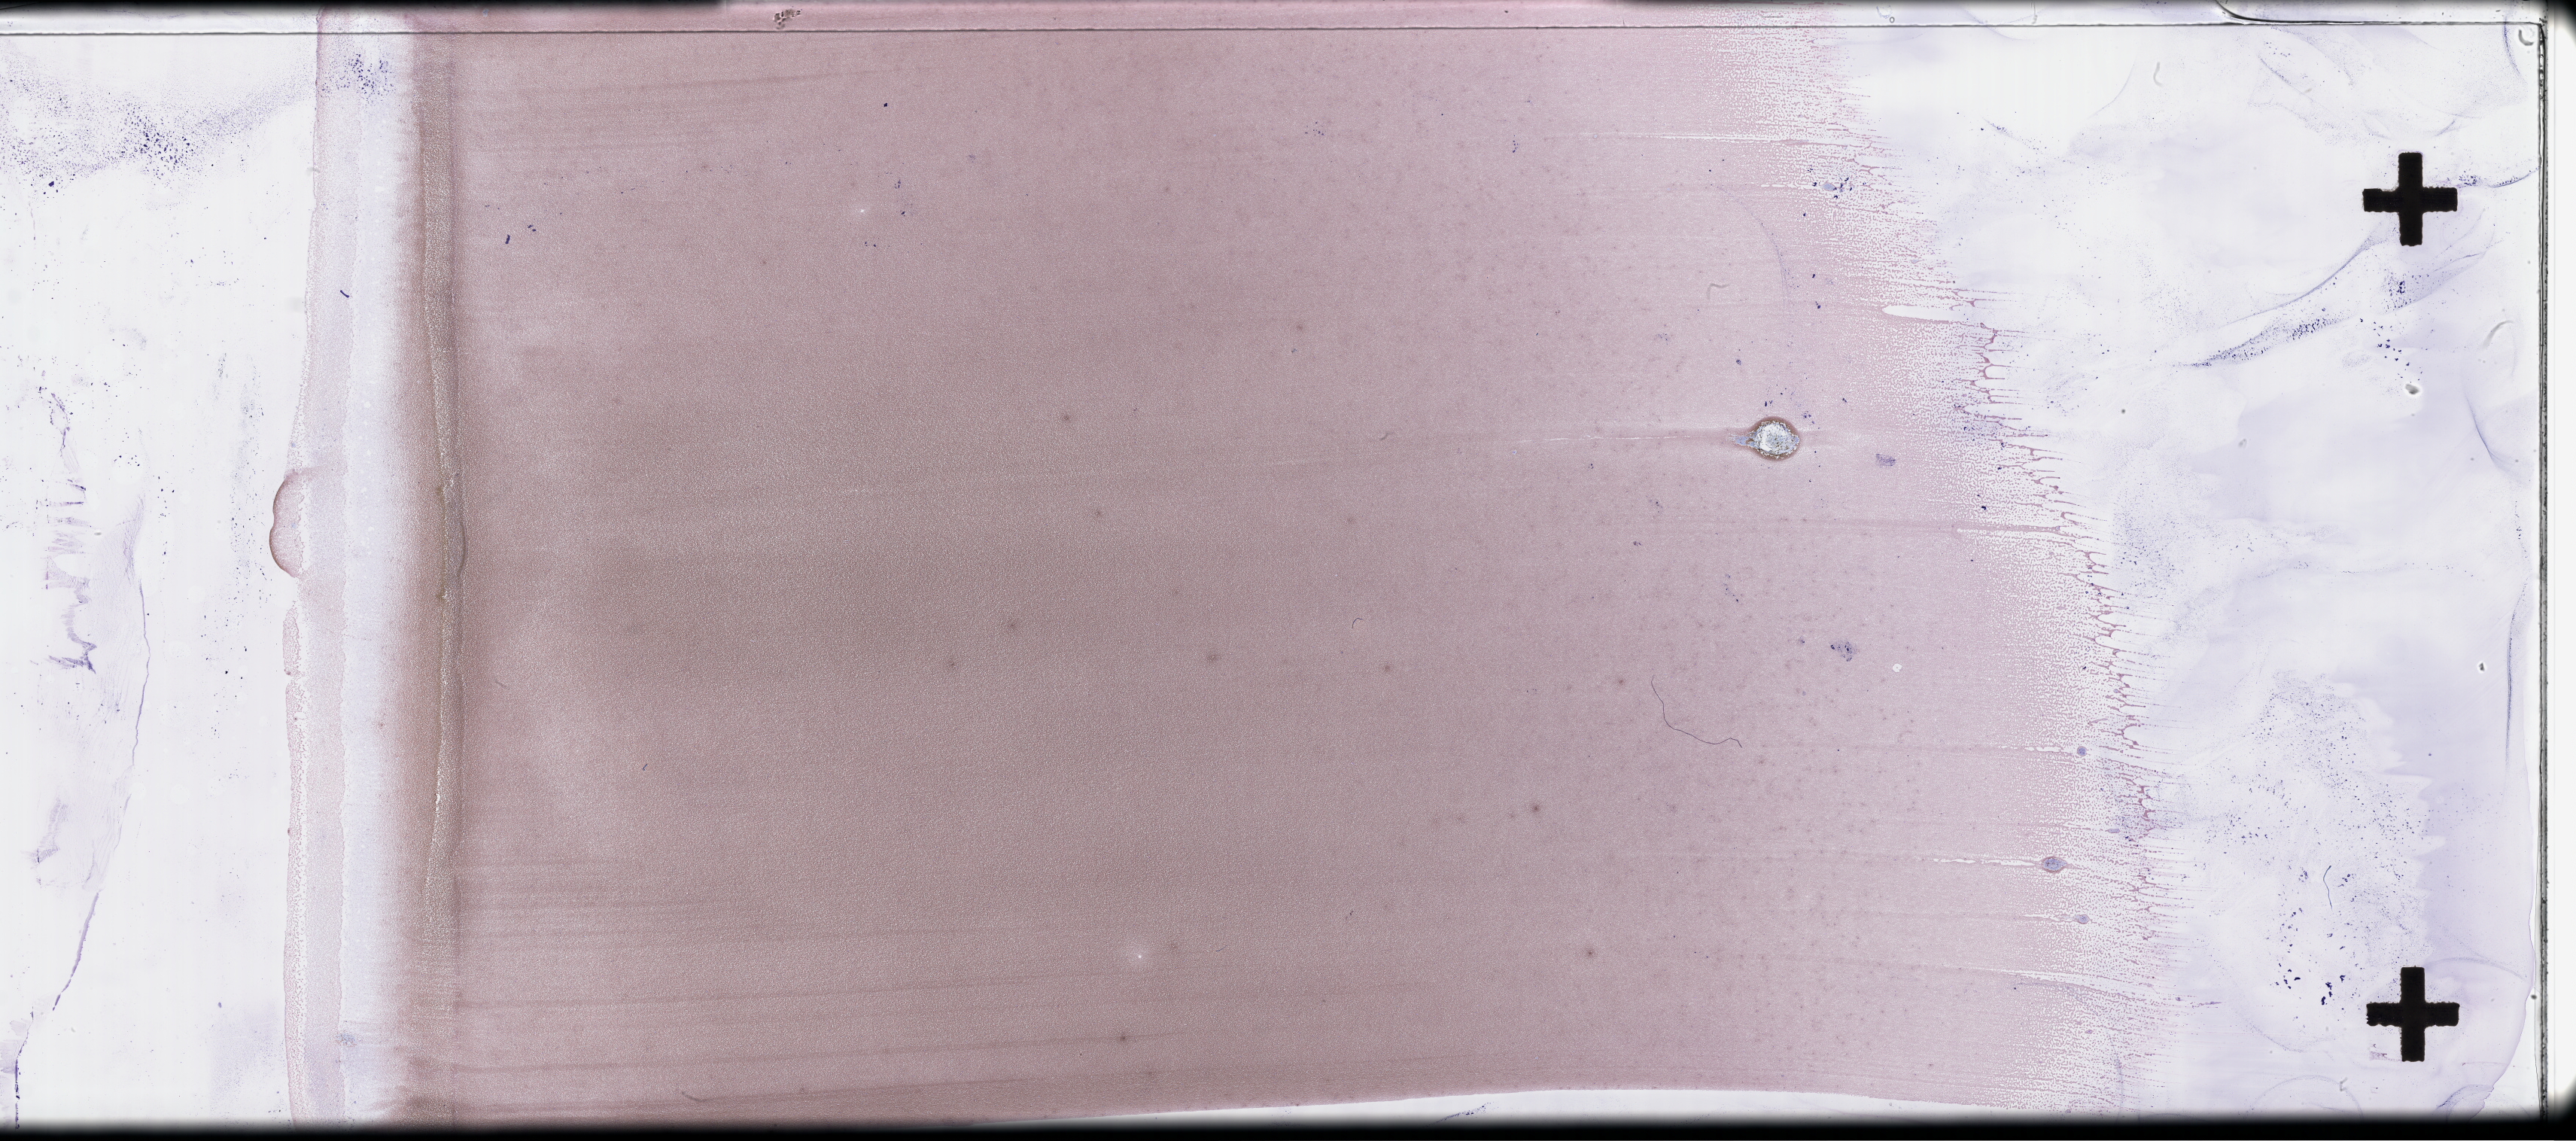
Wright–Giemsa-stained whole blood smear, whole-slide image, whole scanned area (about 55.3 x 24.5 mm) shown as a low-resolution overview; EDTA-anticoagulated smear; collected at disease progression. Patient sex: male.
• patient diagnosis: Plasma Cell Myeloma